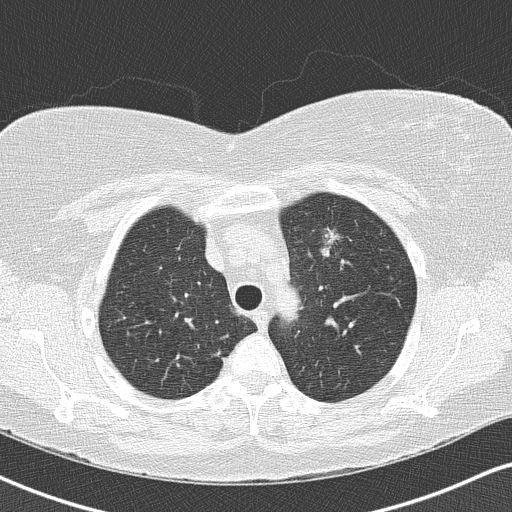
Chest CT (low-dose screening protocol), one axial image. Second screening round (one year after baseline). Lung window (W 1500 / L -600 HU). 2 mm slice thickness. Lung (sharp) reconstruction kernel (B50f). Female, age 57 years at enrolment. Current smoker at enrolment.
Expert-annotated lung lesion, bounding box (x1, y1, x2, y2) in pixels: (312, 220, 351, 264). The screening reader recorded 3 non-calcified nodules or masses ≥4 mm on this exam (left upper lobe, right upper lobe, right middle lobe); which of them this box marks is not recorded. Official screen result: positive, other. Lung cancer was diagnosed 75 days after this screen: adenocarcinoma, NOS, left upper lobe, poorly differentiated (G3), stage IA (AJCC 6th edition), 24 mm at pathology.